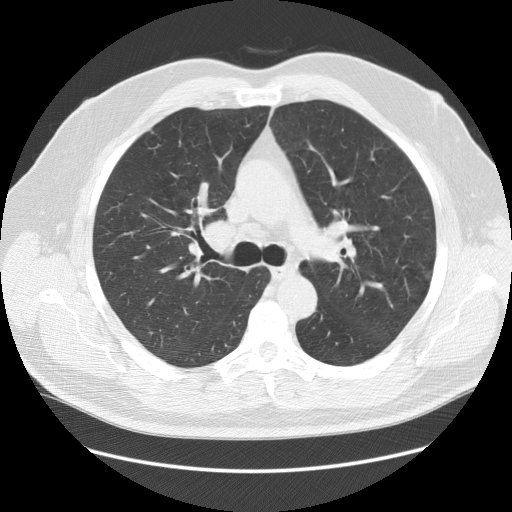
Chest CT (low-dose screening protocol), one axial image, baseline screening round, lung window (W 1500 / L -600 HU), 2.5 mm slice thickness, standard (soft-tissue) reconstruction kernel (STANDARD), slice 49 of 140 in the series, 512 × 512 image matrix. Male participant, aged 64 years at enrolment.
Expert-annotated lung lesion, bounding box [x1, y1, x2, y2] px = [179, 206, 251, 273]. Reader record for this screening exam (exam-level; its link to the box is not recorded): non-calcified nodule or mass ≥4 mm, right lower lobe, 7 × 5 mm, smooth margins, soft tissue attenuation. Lung cancer was diagnosed 456 days after this screen (after the second annual screen): adenocarcinoma, NOS, right upper lobe, poorly differentiated (G3), stage IB (AJCC 6th edition), 37 mm at pathology.